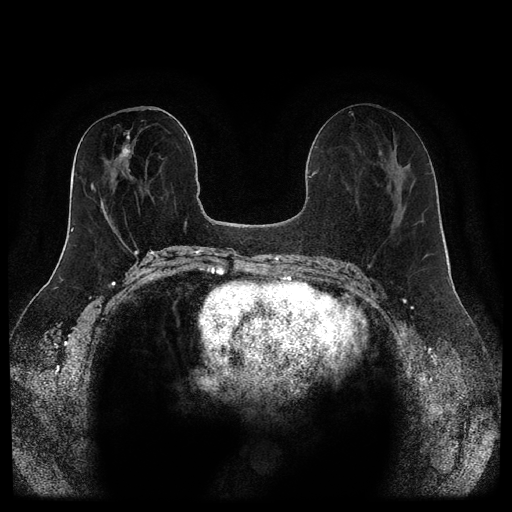
Breast MRI (dynamic contrast-enhanced, multi-phase), one axial slice. Slice 49 of 116 in the series (ordered by position). Dynamic contrast-enhanced series, time point 2 of 5 at this slice position (early post-contrast). 1.5 T. TE 2.6 ms, TR 5.3 ms. 2 mm slice thickness. 512 × 512 image matrix. Female patient, age 46 years.
Annotated regions visible in this slice (semi-automatically segmented with operator editing):
- breast lesion (labelled 'tumour' in the annotation; benign lesions carry a separate 'benign' label): bounding box [x1, y1, x2, y2] px = [115, 130, 133, 169]